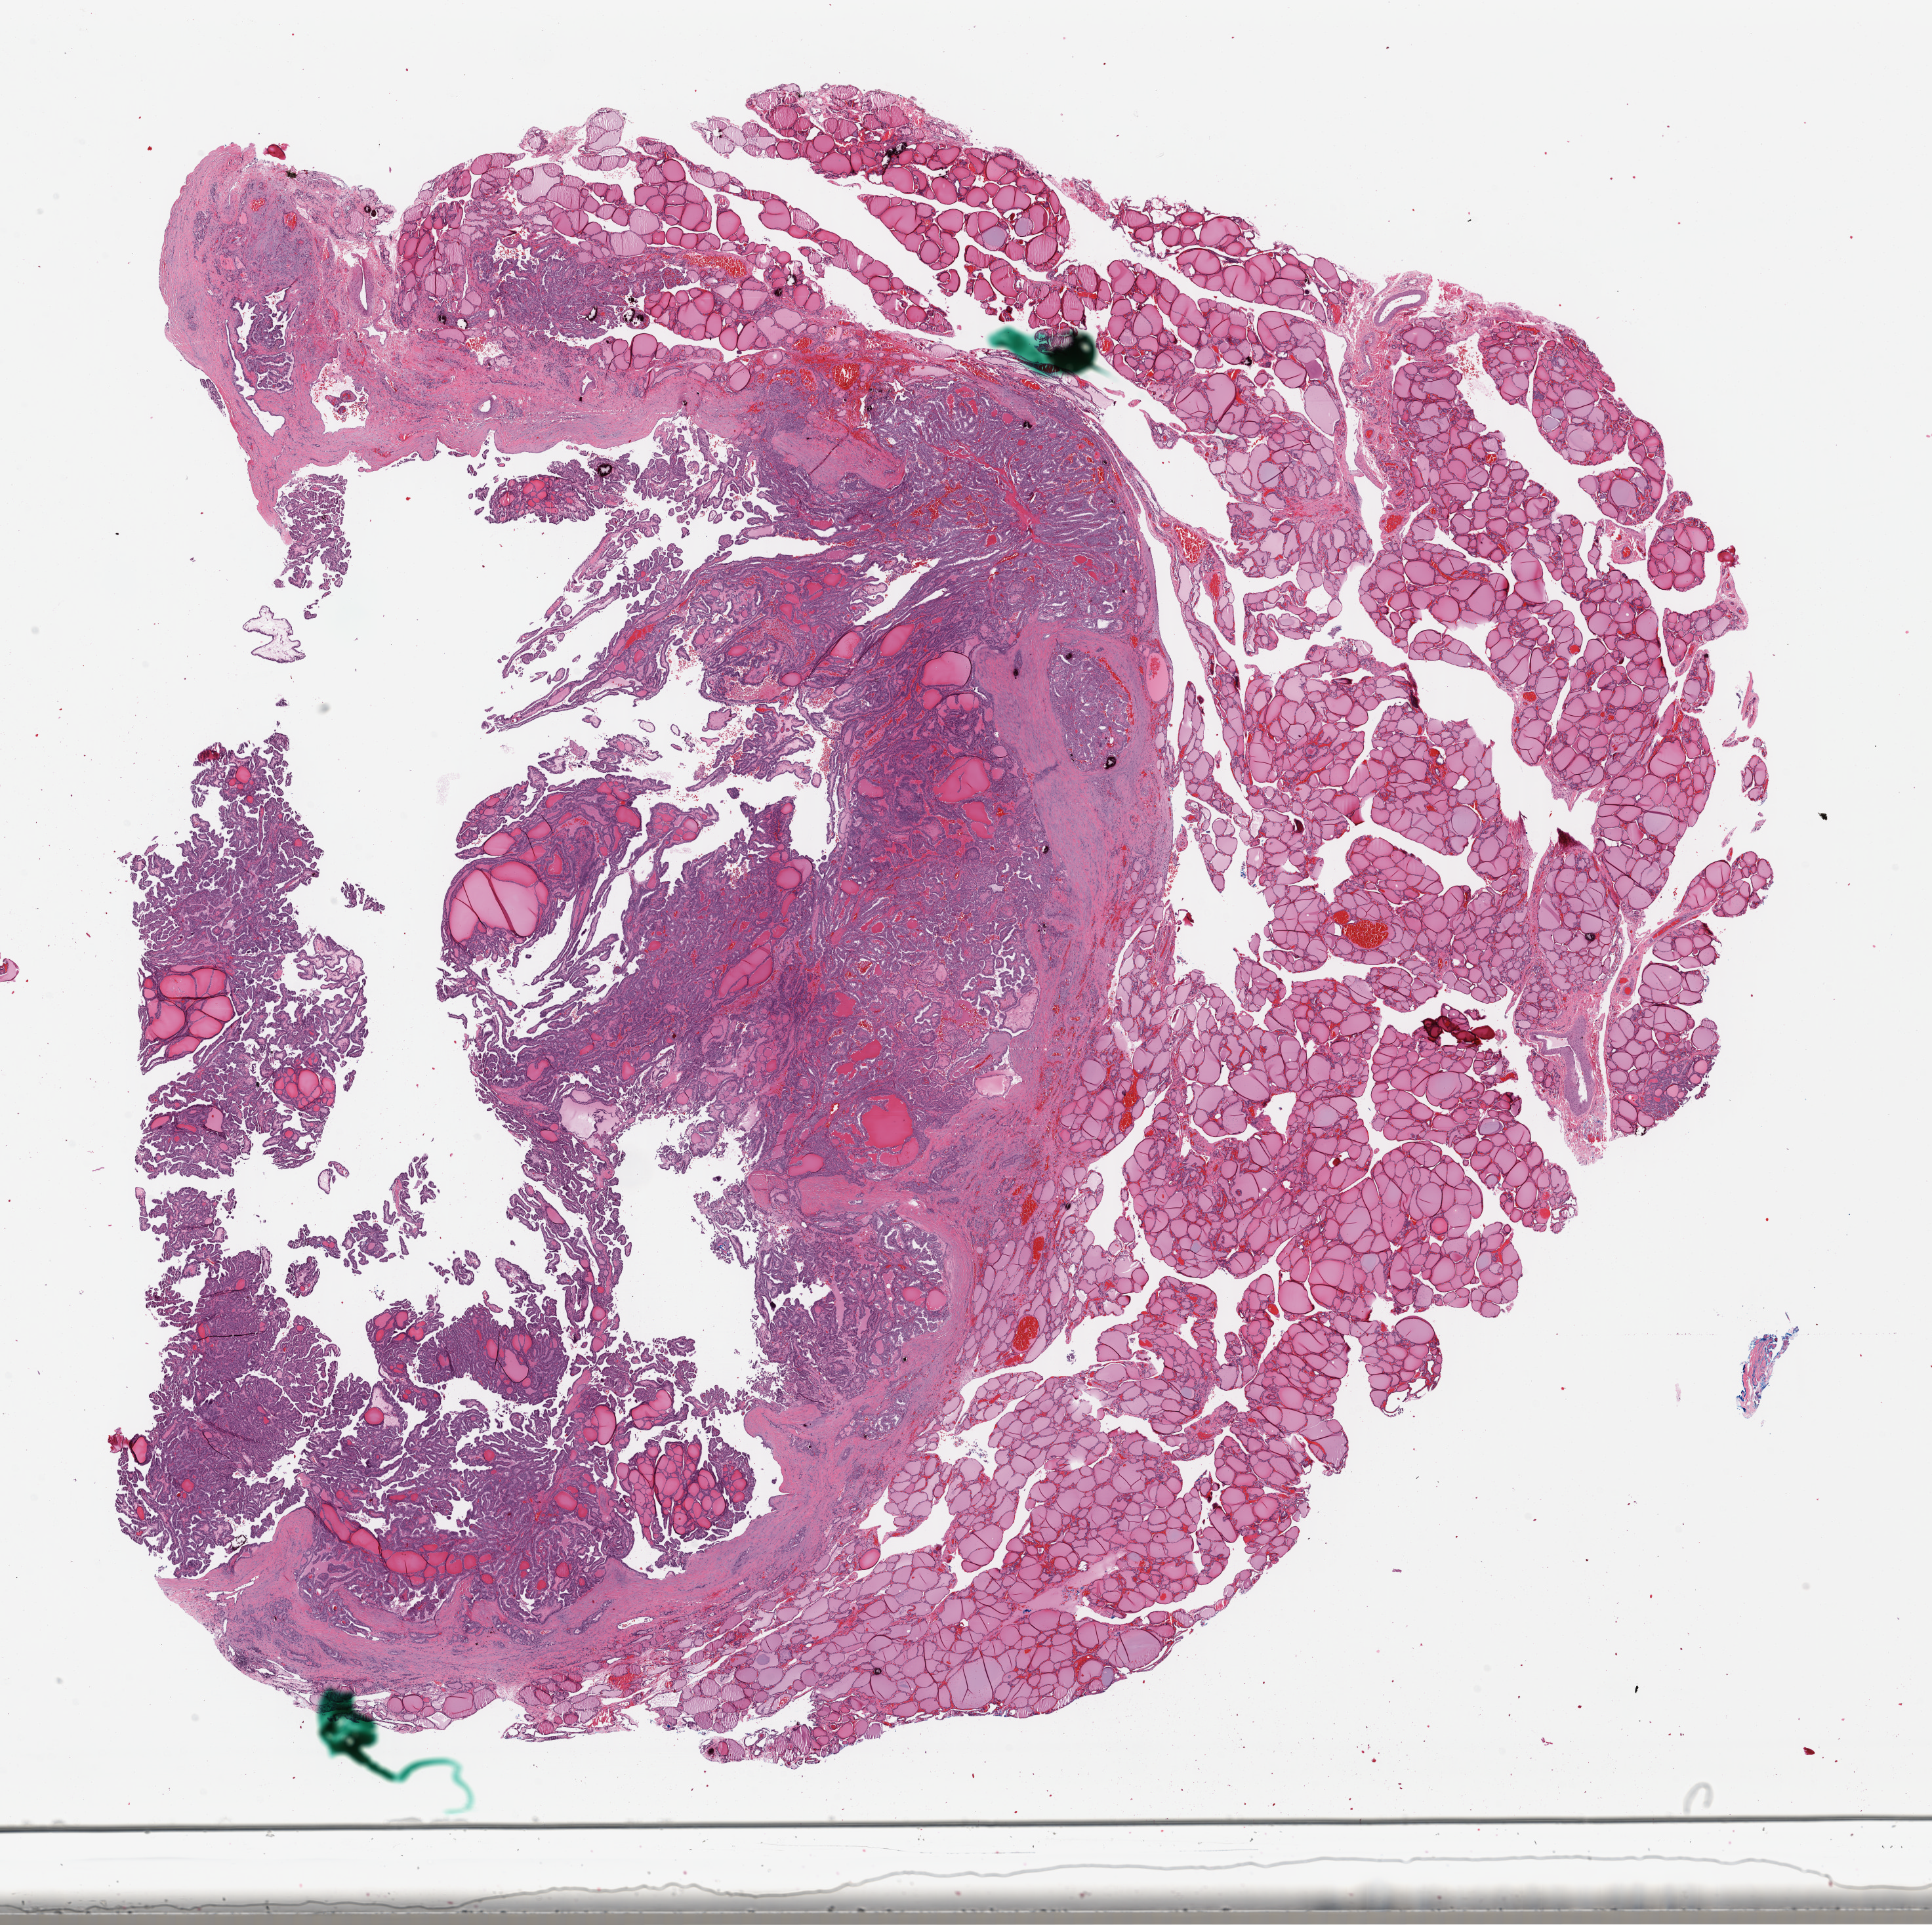
H&E-stained whole-slide image, whole scanned area (about 23.1 x 23.1 mm) shown as a low-resolution overview; formalin-fixed paraffin-embedded (FFPE) diagnostic section; thyroid, primary tumour sample. Male patient; age at initial diagnosis 26 years.
Lymph nodes positive (case pathology): 7 of 12 examined. AJCC pathologic stage: I (7th edition). Diagnosis: Papillary adenocarcinoma, NOS (thyroid gland).